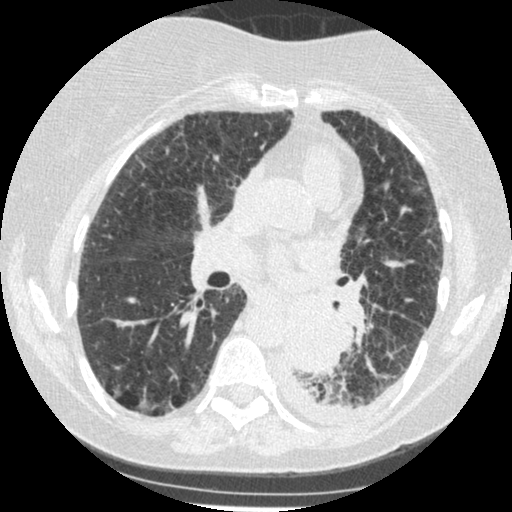
Low-dose screening chest CT, one axial slice; slice 131 of 341 in the series (ordered by position); reconstruction kernel STANDARD; 120 kVp; lung window (W 1500 / L -600 HU); 1.25 mm slice thickness; 512 × 512 image matrix.
Structures marked on this image (outlined manually by an expert reader):
- lesion 1 (tumor, lower lobe of left lung): bounding box <285,306,346,375> (left, top, right, bottom; pixels)